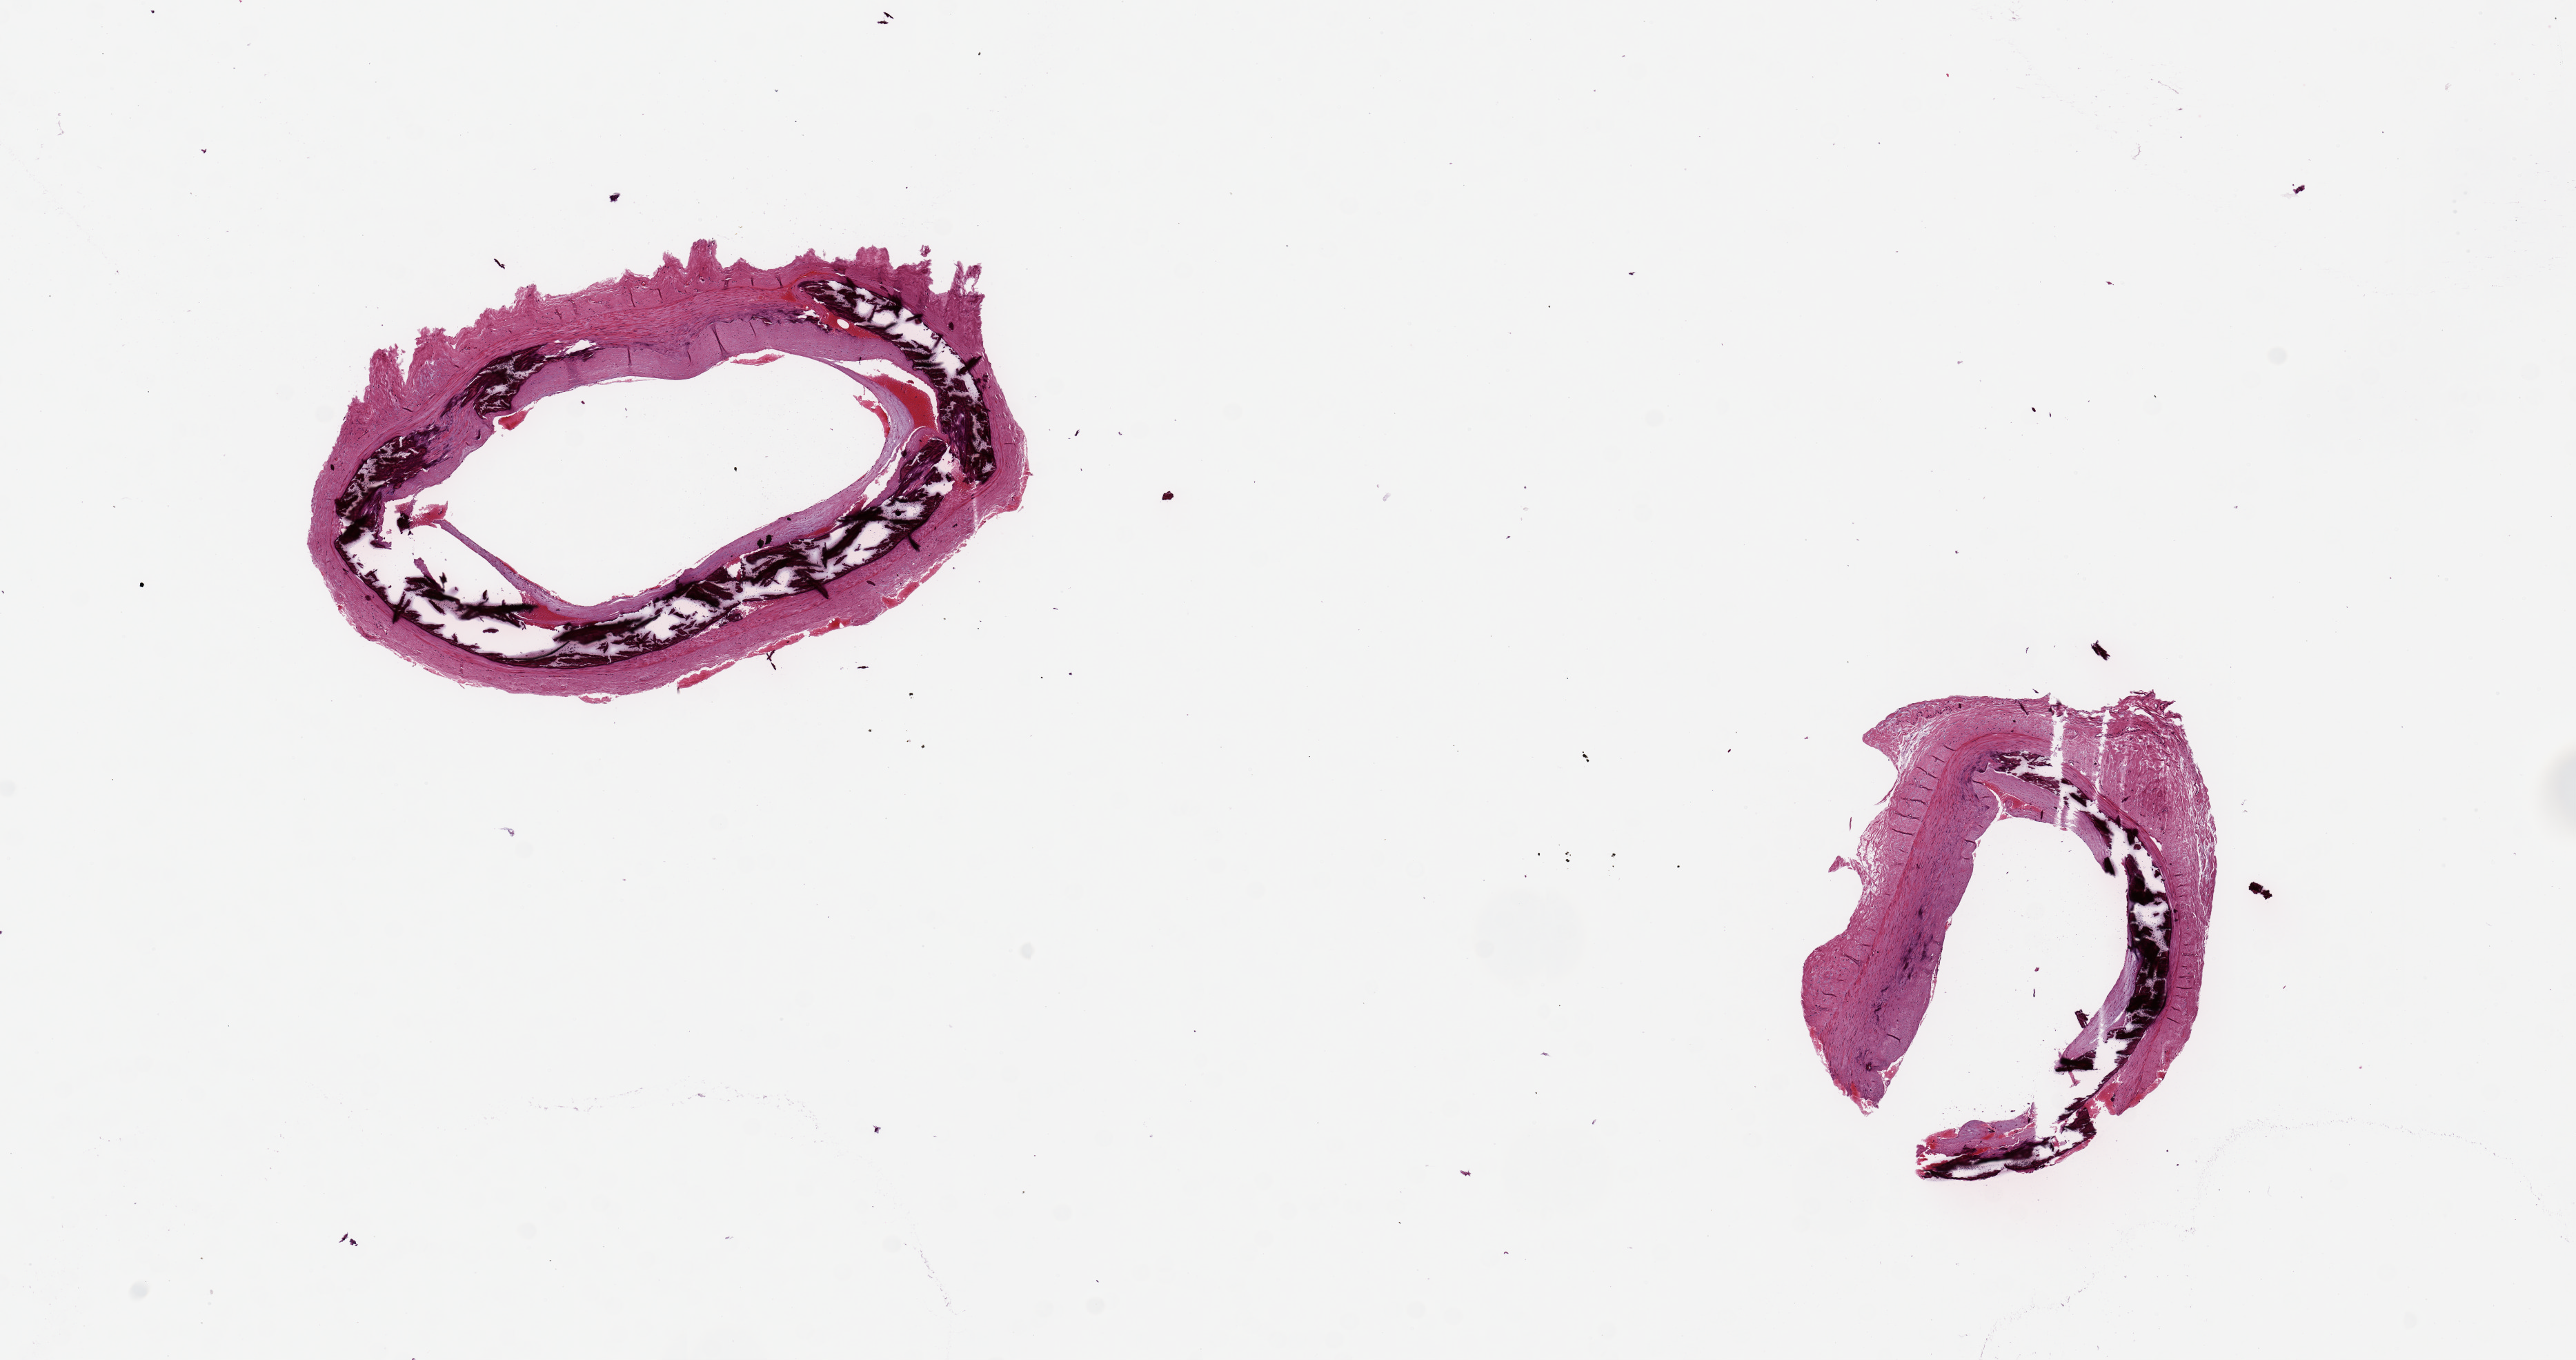
H&E whole-slide image — whole scanned area (about 14.8 x 7.8 mm, slide scanned at 20x) shown as a low-resolution overview, PAXgene-fixed, paraffin-embedded tissue, section of tibial artery (target tissue), donor tissue sample. Donor sex: male.
Review note (as recorded): 2 pieces, 3x2 & 4x2mm; extensive medial calcification.